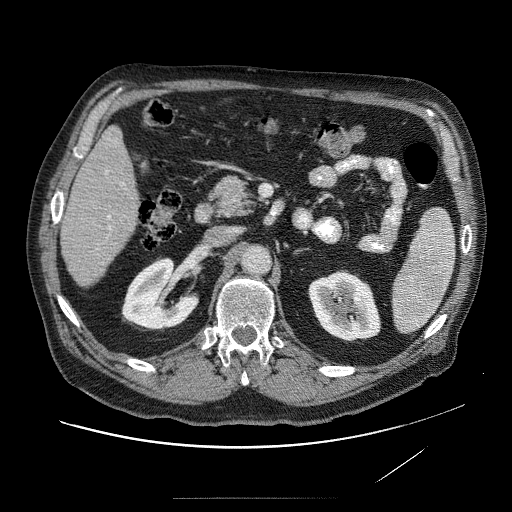
Contrast-enhanced abdominal CT (liver protocol), one axial slice; slice 25 of 89 in the series (ordered by position); reconstruction kernel STANDARD; 120 kVp; soft-tissue window (W 400 / L 40 HU); 2.5 mm slice thickness; 512 × 512 image matrix. From the clinical record (not read from this slice): diagnosis: hepatocellular carcinoma (patient treated with transarterial chemoembolisation; whether this scan precedes or follows treatment is not stated here); TNM stage (as recorded): Stage-IVA.
Annotated regions visible in this slice (semi-automatically segmented with operator editing):
- liver parenchyma outside the tumour (the mass and vessels are separate outlines, so this box may not span the whole liver): box from (x=60, y=122) to (x=146, y=290) px
- liver vessels: (x=112, y=183)–(x=131, y=225)